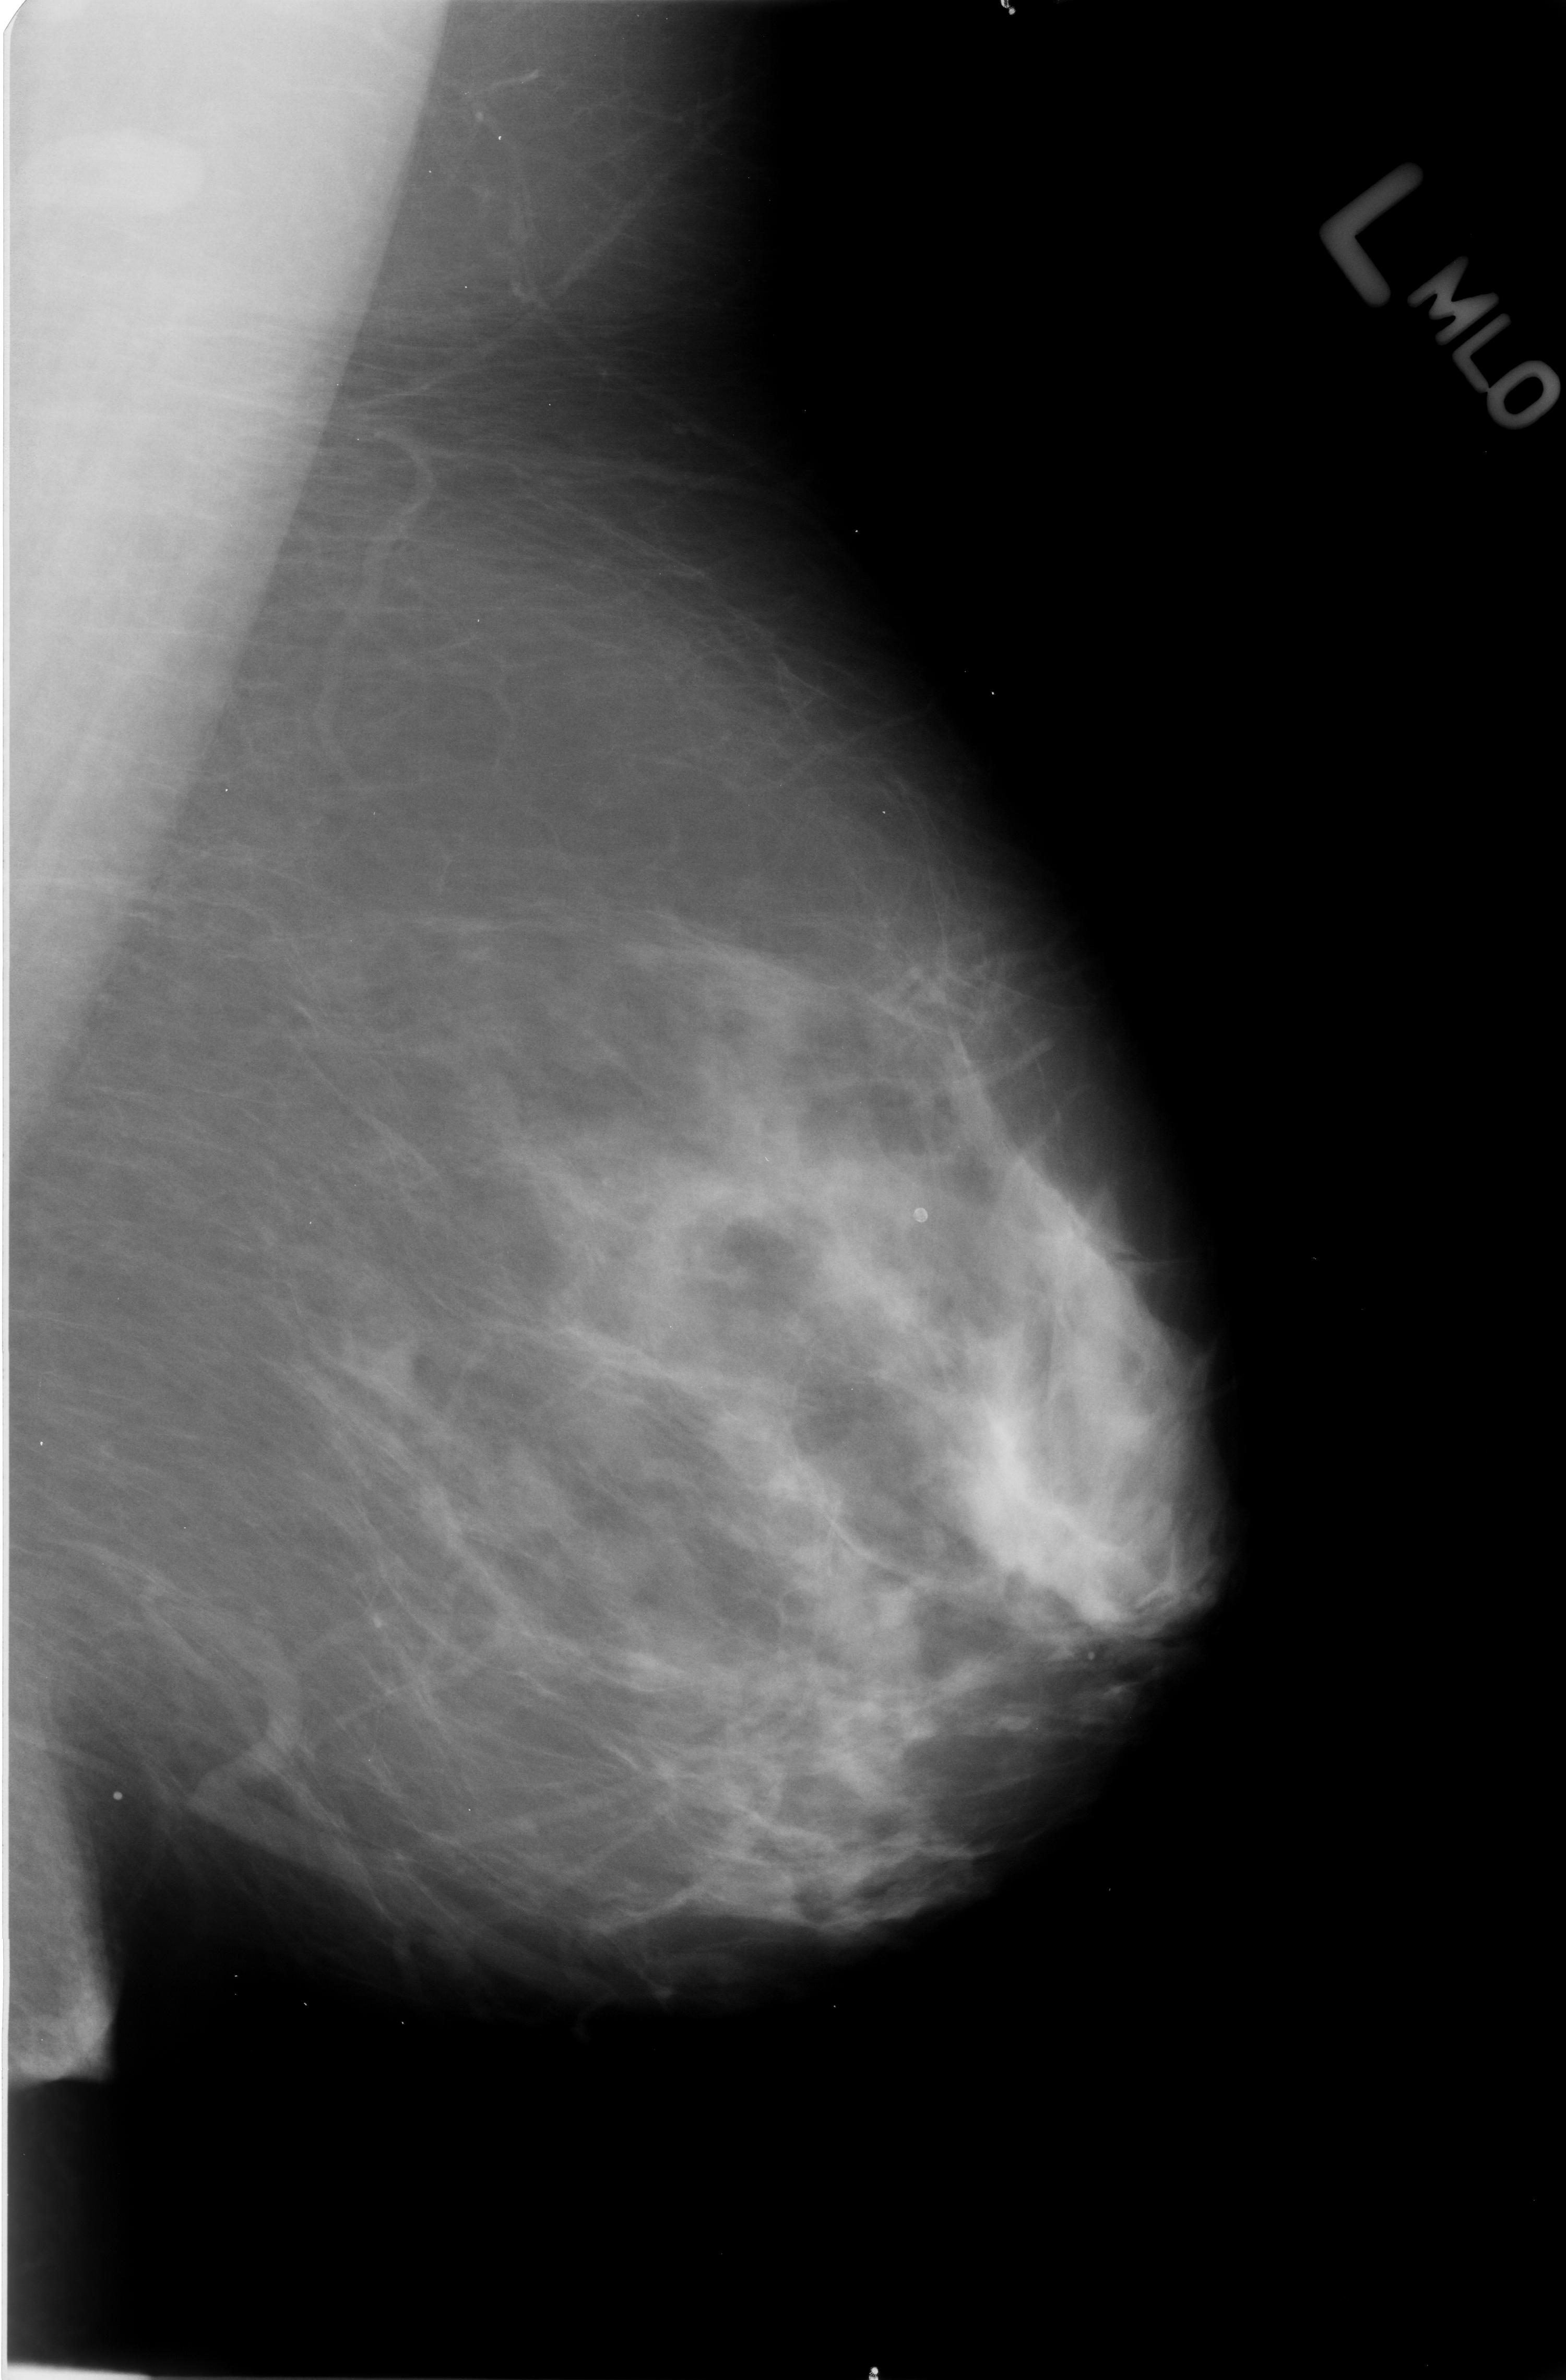
Mammogram (digitized film), left breast, MLO view.
Marked abnormality: calcifications, morphology lucent center; BI-RADS assessment category 2; benign without callback (not worked up further).